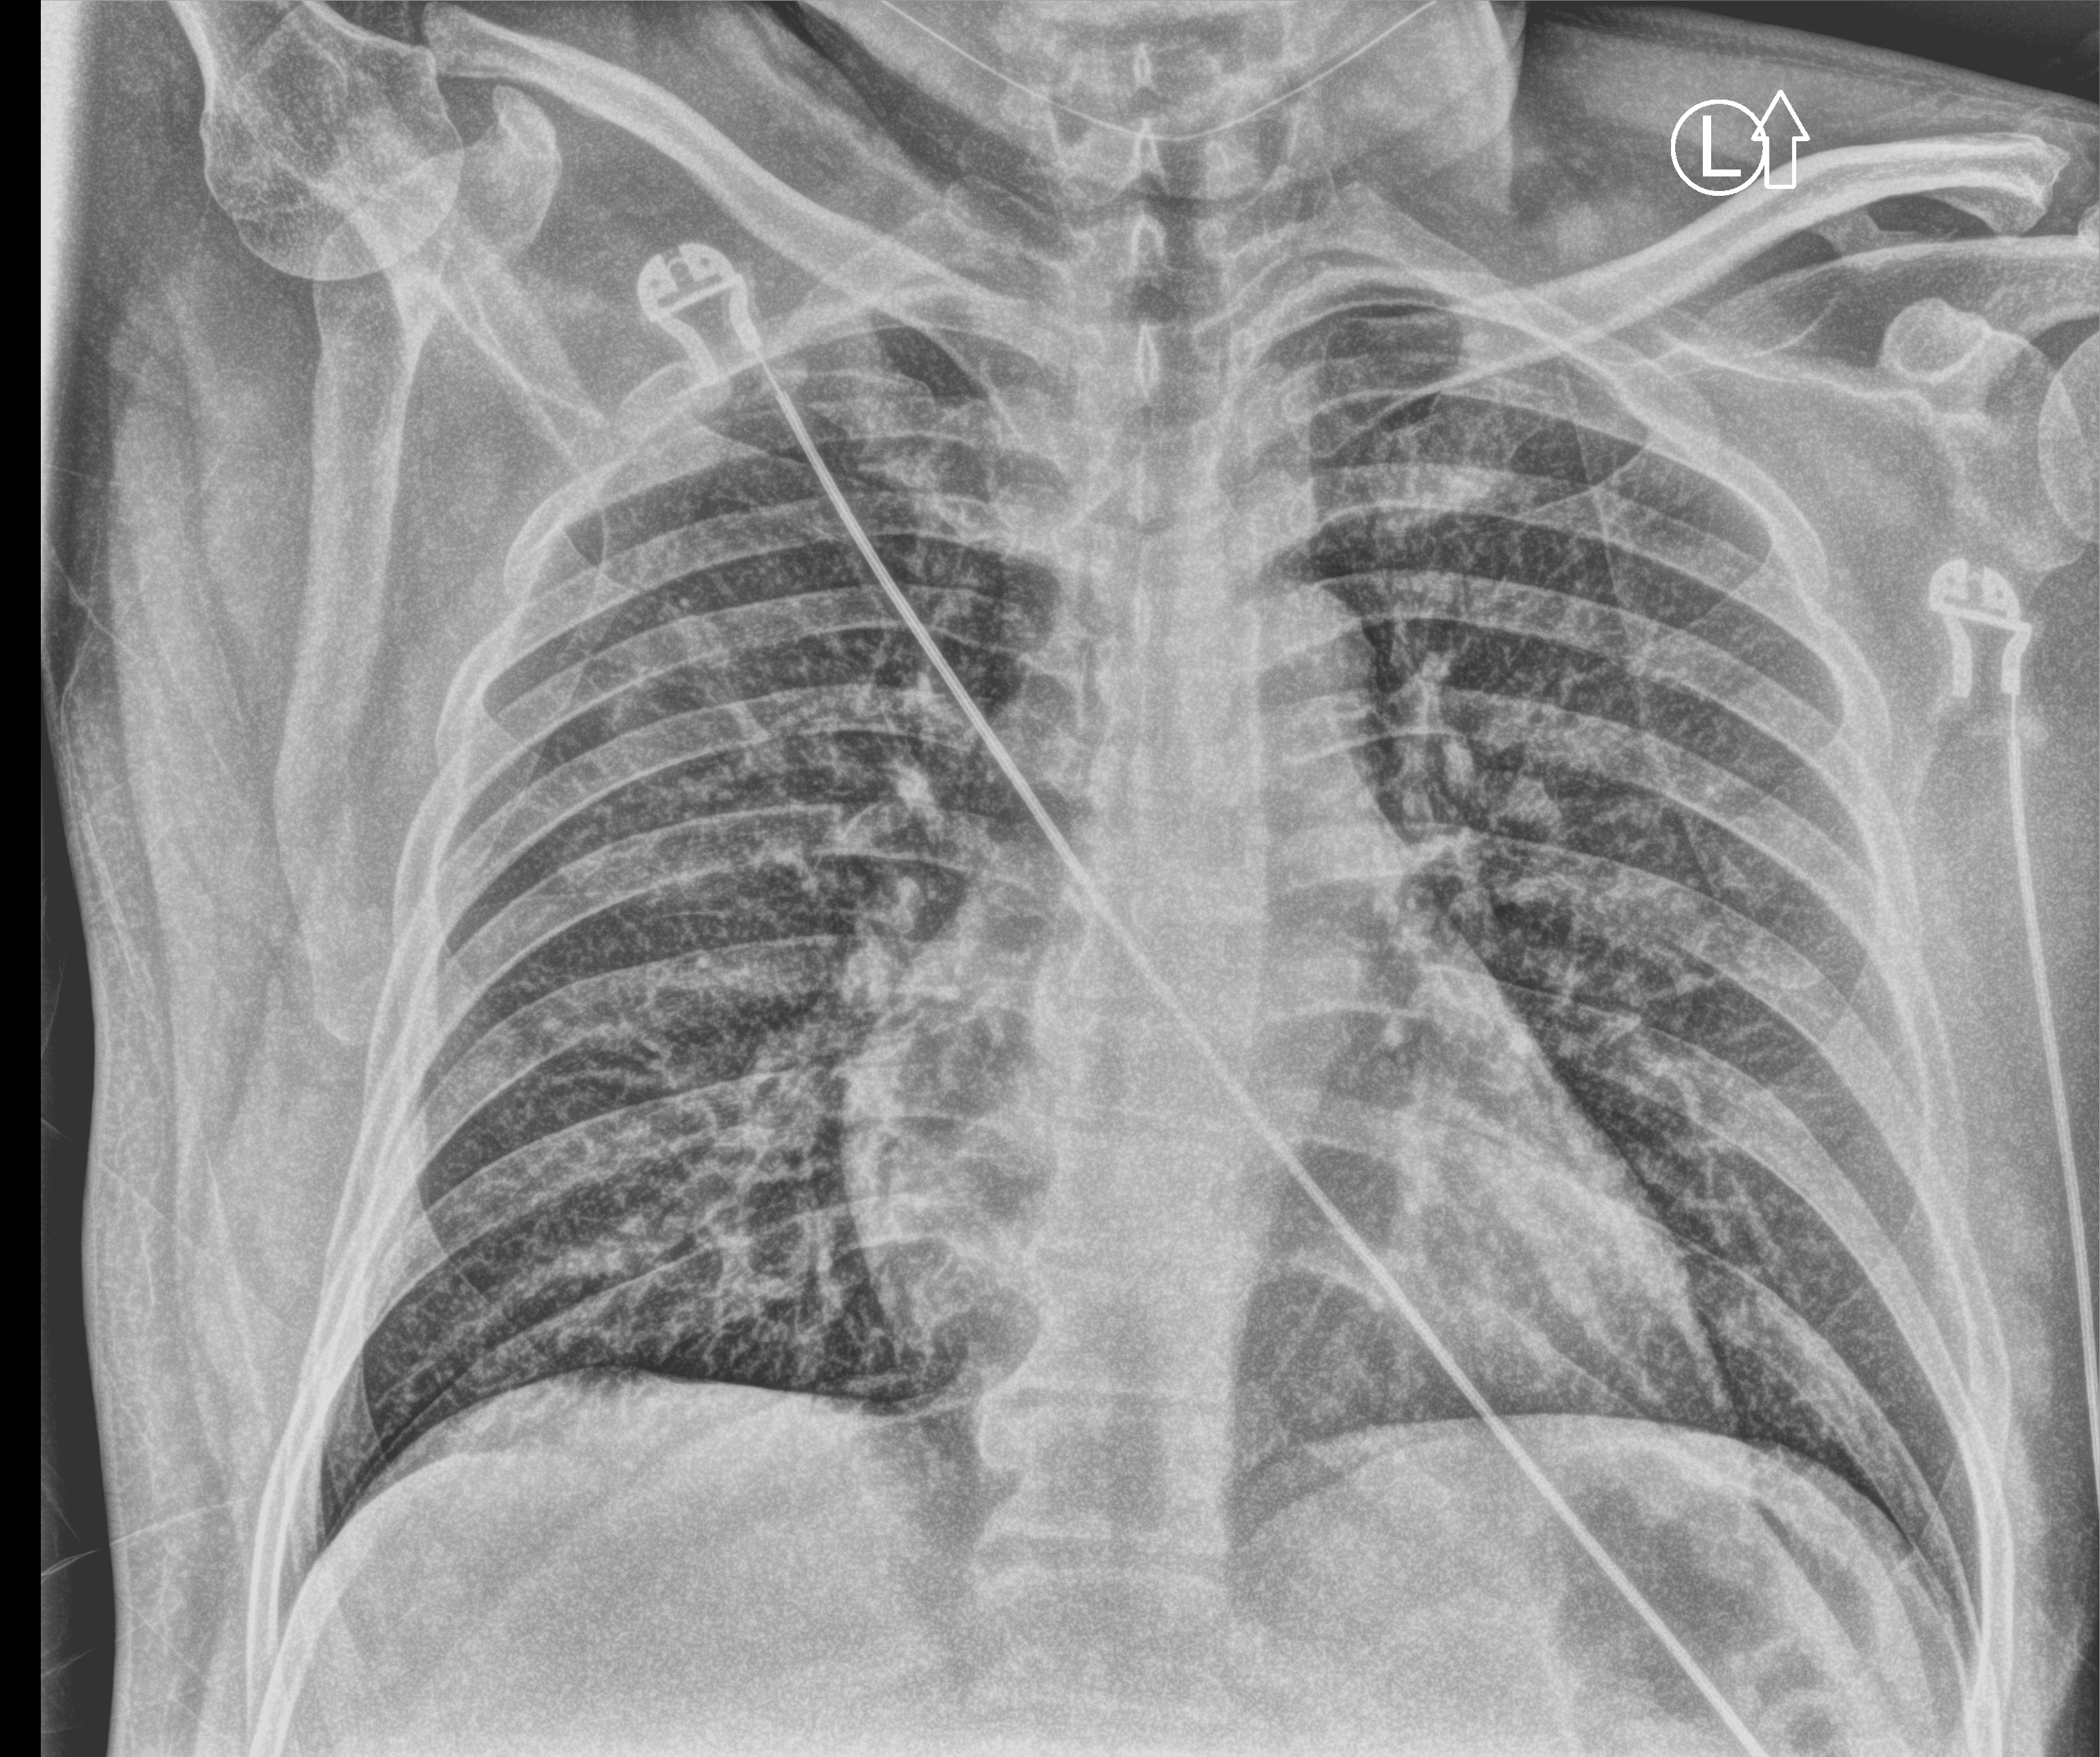
Portable chest radiograph. Male patient hospitalised with COVID-19, age 18–59 years.
Admission-level facts for this patient (not findings on this image; timing relative to this image not recorded): smoking status (admission record): never; mechanically ventilated during this hospital stay: no.